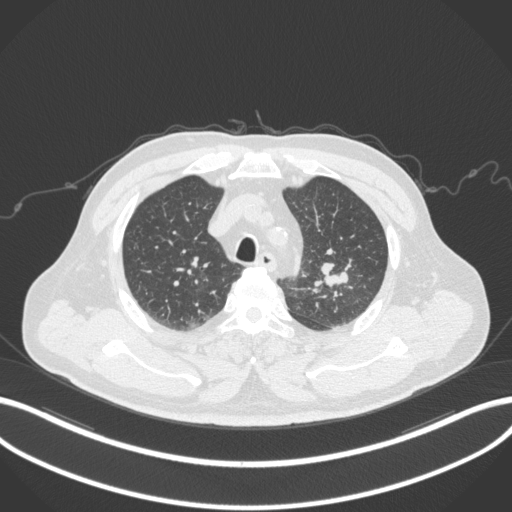
Chest CT, one axial slice. Slice 238 of 286 in the series (ordered by position). Reconstruction kernel B31f. 120 kVp. Lung window (W 1500 / L -600 HU). 512 × 512 image matrix. Male patient, age 67 years. Case-level facts recorded for this patient, not image findings: clinical TNM (as recorded): T2a N1 M0.
Structures marked on this image (bounding box drawn by a radiologist):
- lung tumour (recorded histology: adenocarcinoma): bounding box [x1, y1, x2, y2] px = [317, 255, 354, 289]